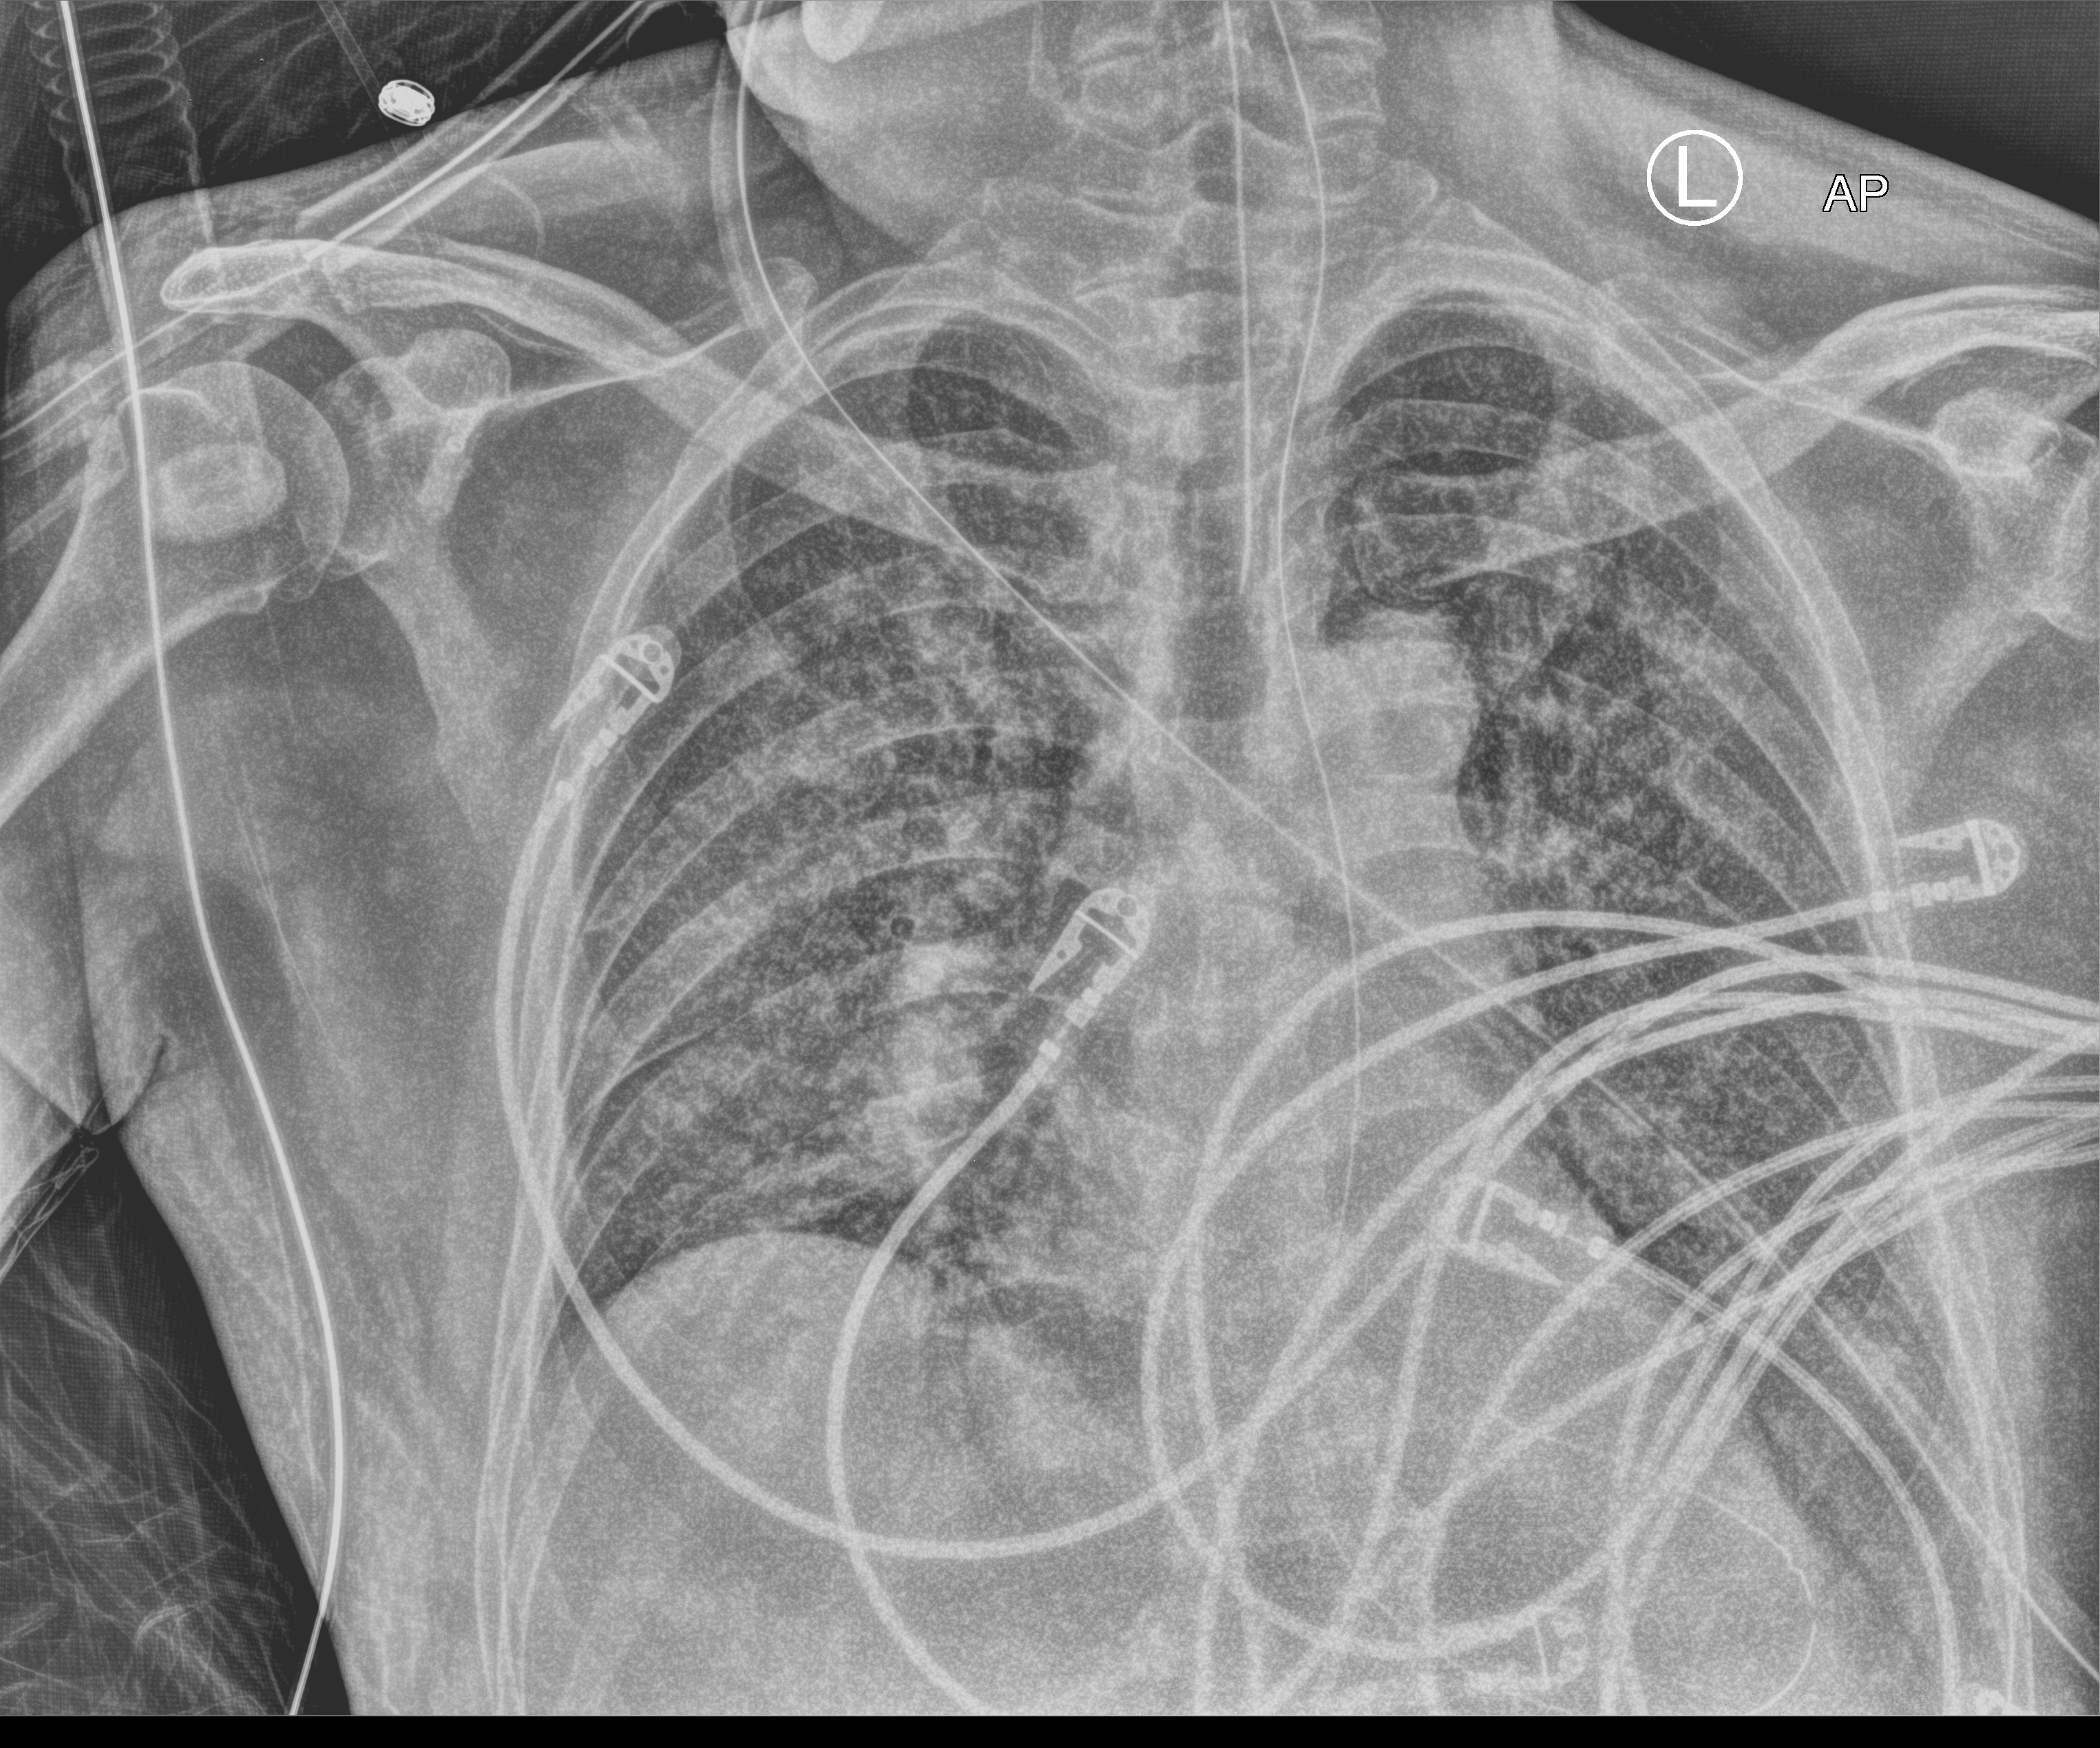
Bedside chest radiograph (computed radiography), anteroposterior (AP) projection. Patient hospitalised with COVID-19; male, aged 60–74 years.
Admission-level facts for this patient (not findings on this image; timing relative to this image not recorded):
- admitted to intensive care during this hospital stay: yes
- length of hospital stay: 14 days
- hypertension (admission record): yes